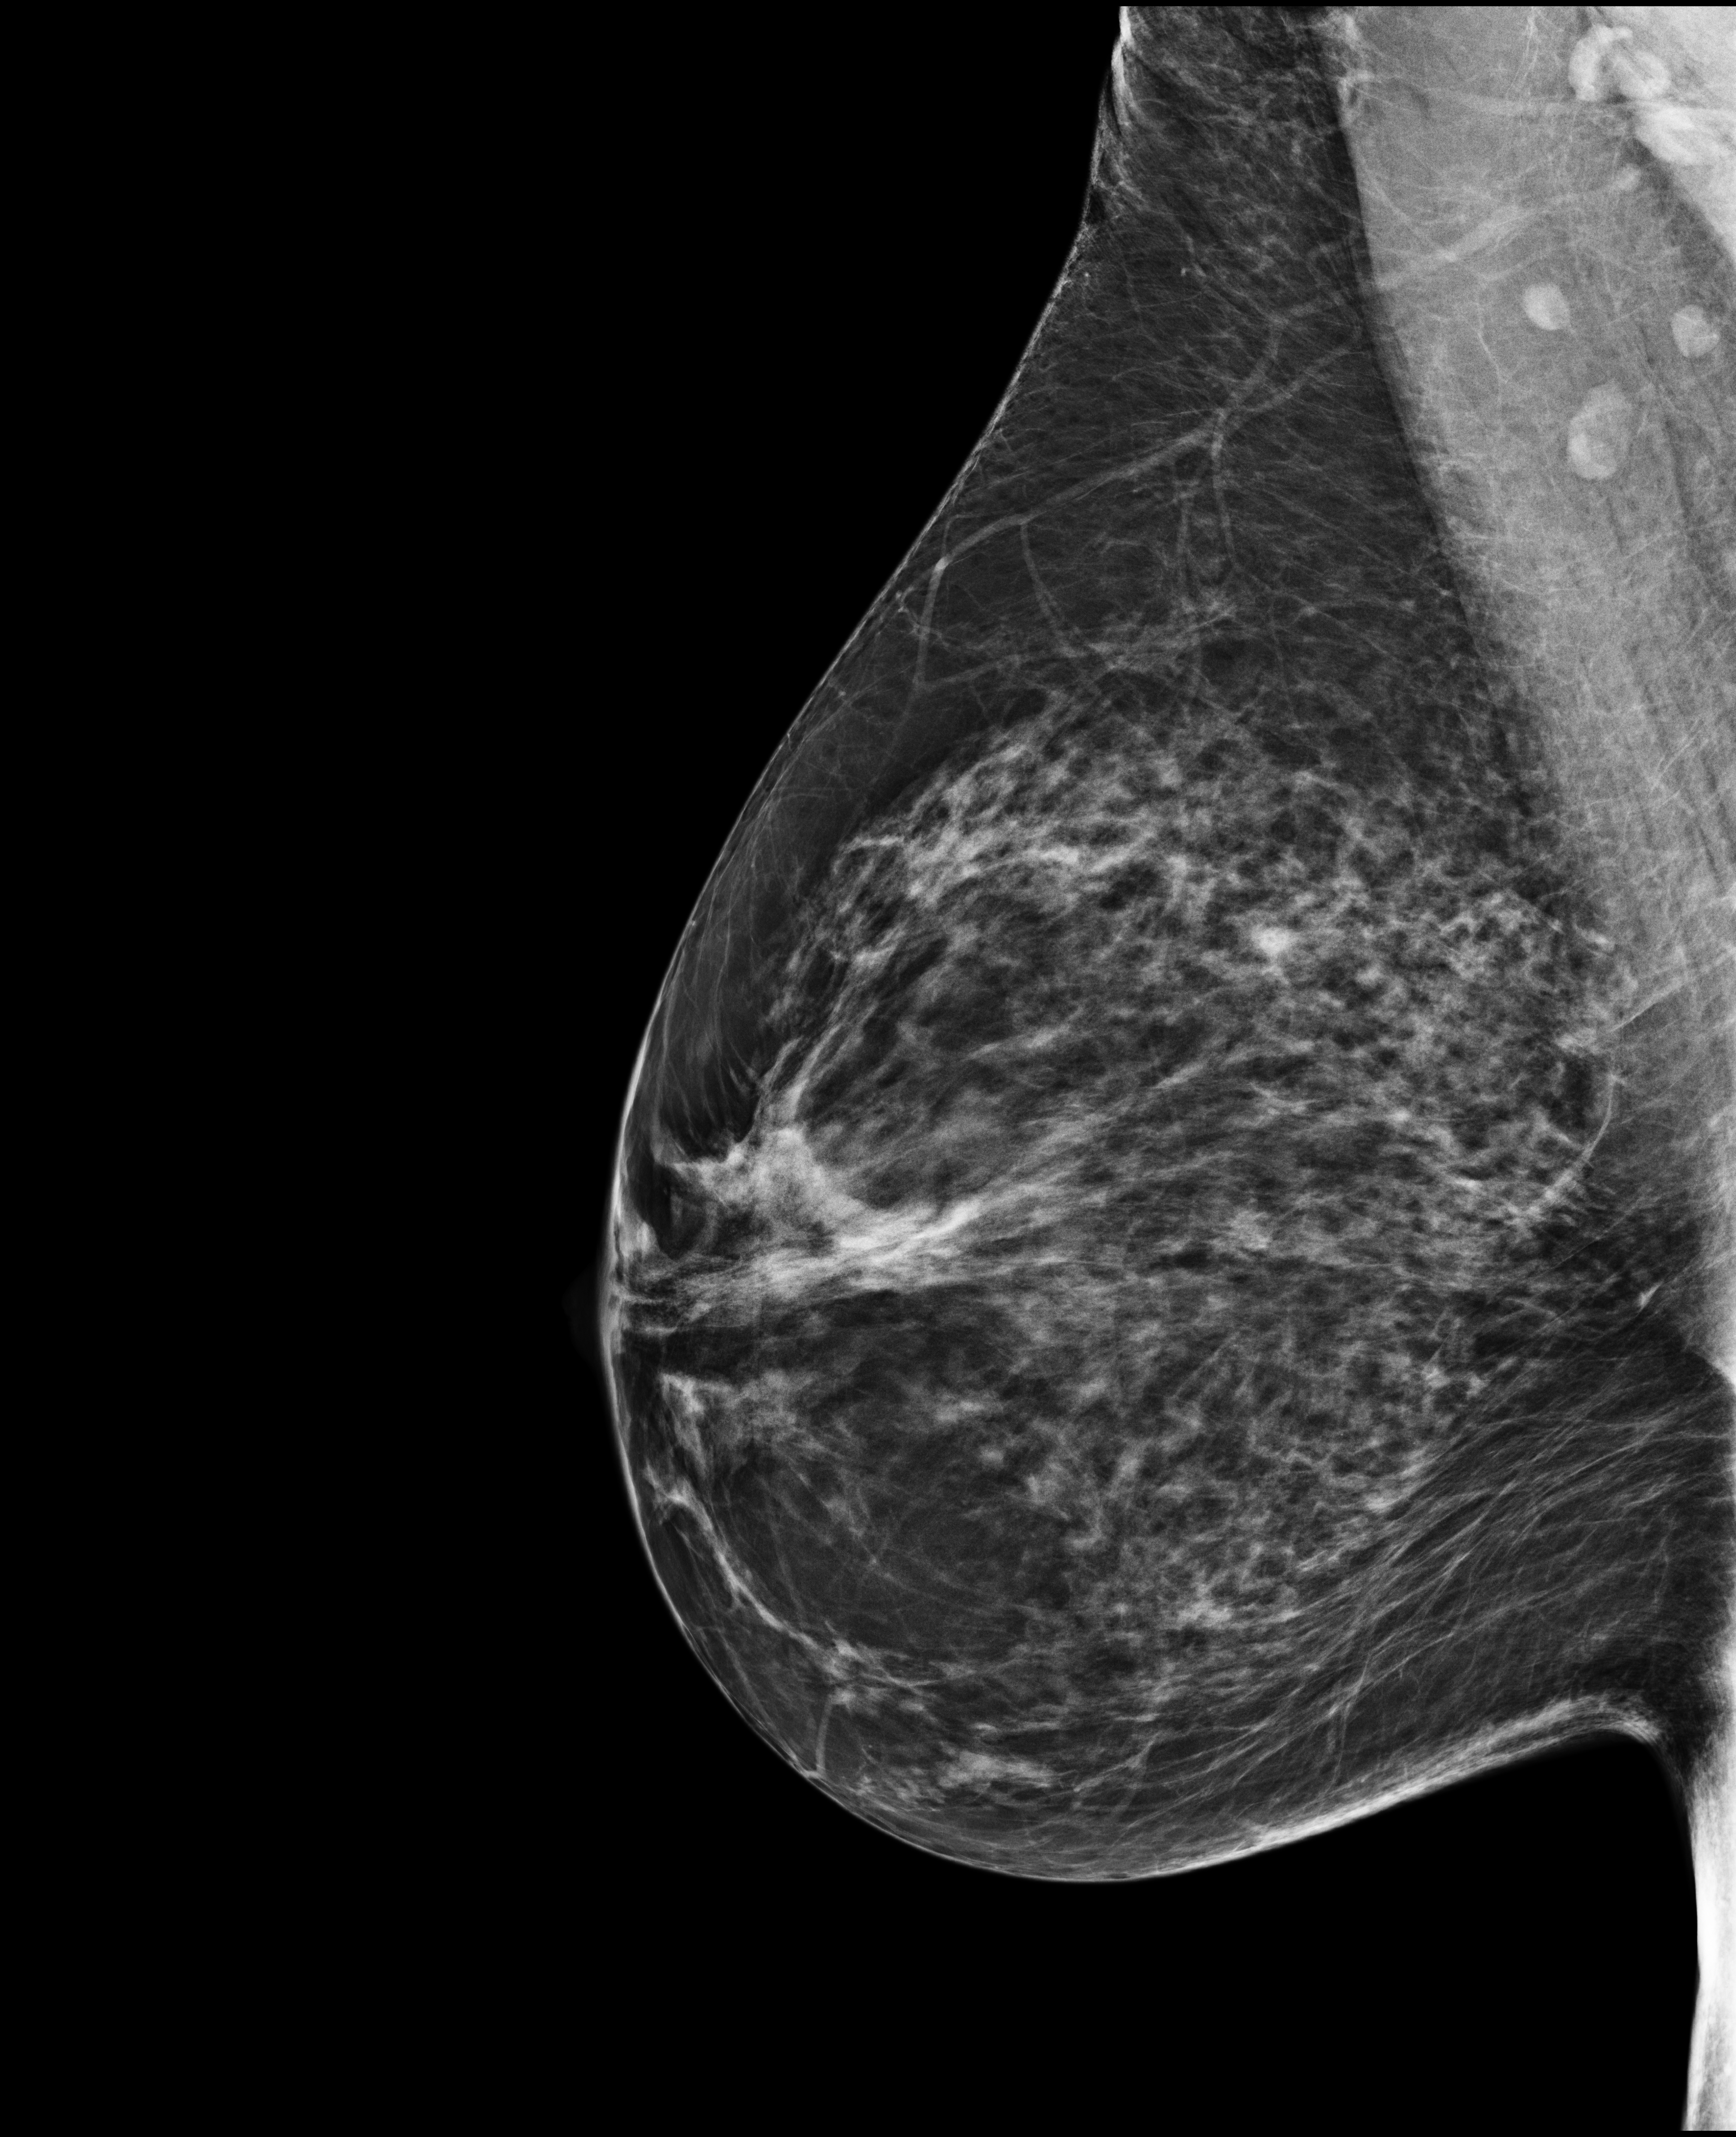
Annual screening mammography examination; system: Selenia Dimensions. Patient aged 61 years (female).
Image type: full-field digital mammogram. Breast: right. Projection: mediolateral oblique (MLO) view. BI-RADS breast density category at the screening exam (both breasts, scale 1–4): 2. Final BI-RADS assessment for this screening round (tomosynthesis exam, both breasts): category 1. Recall: no recall after this screen.